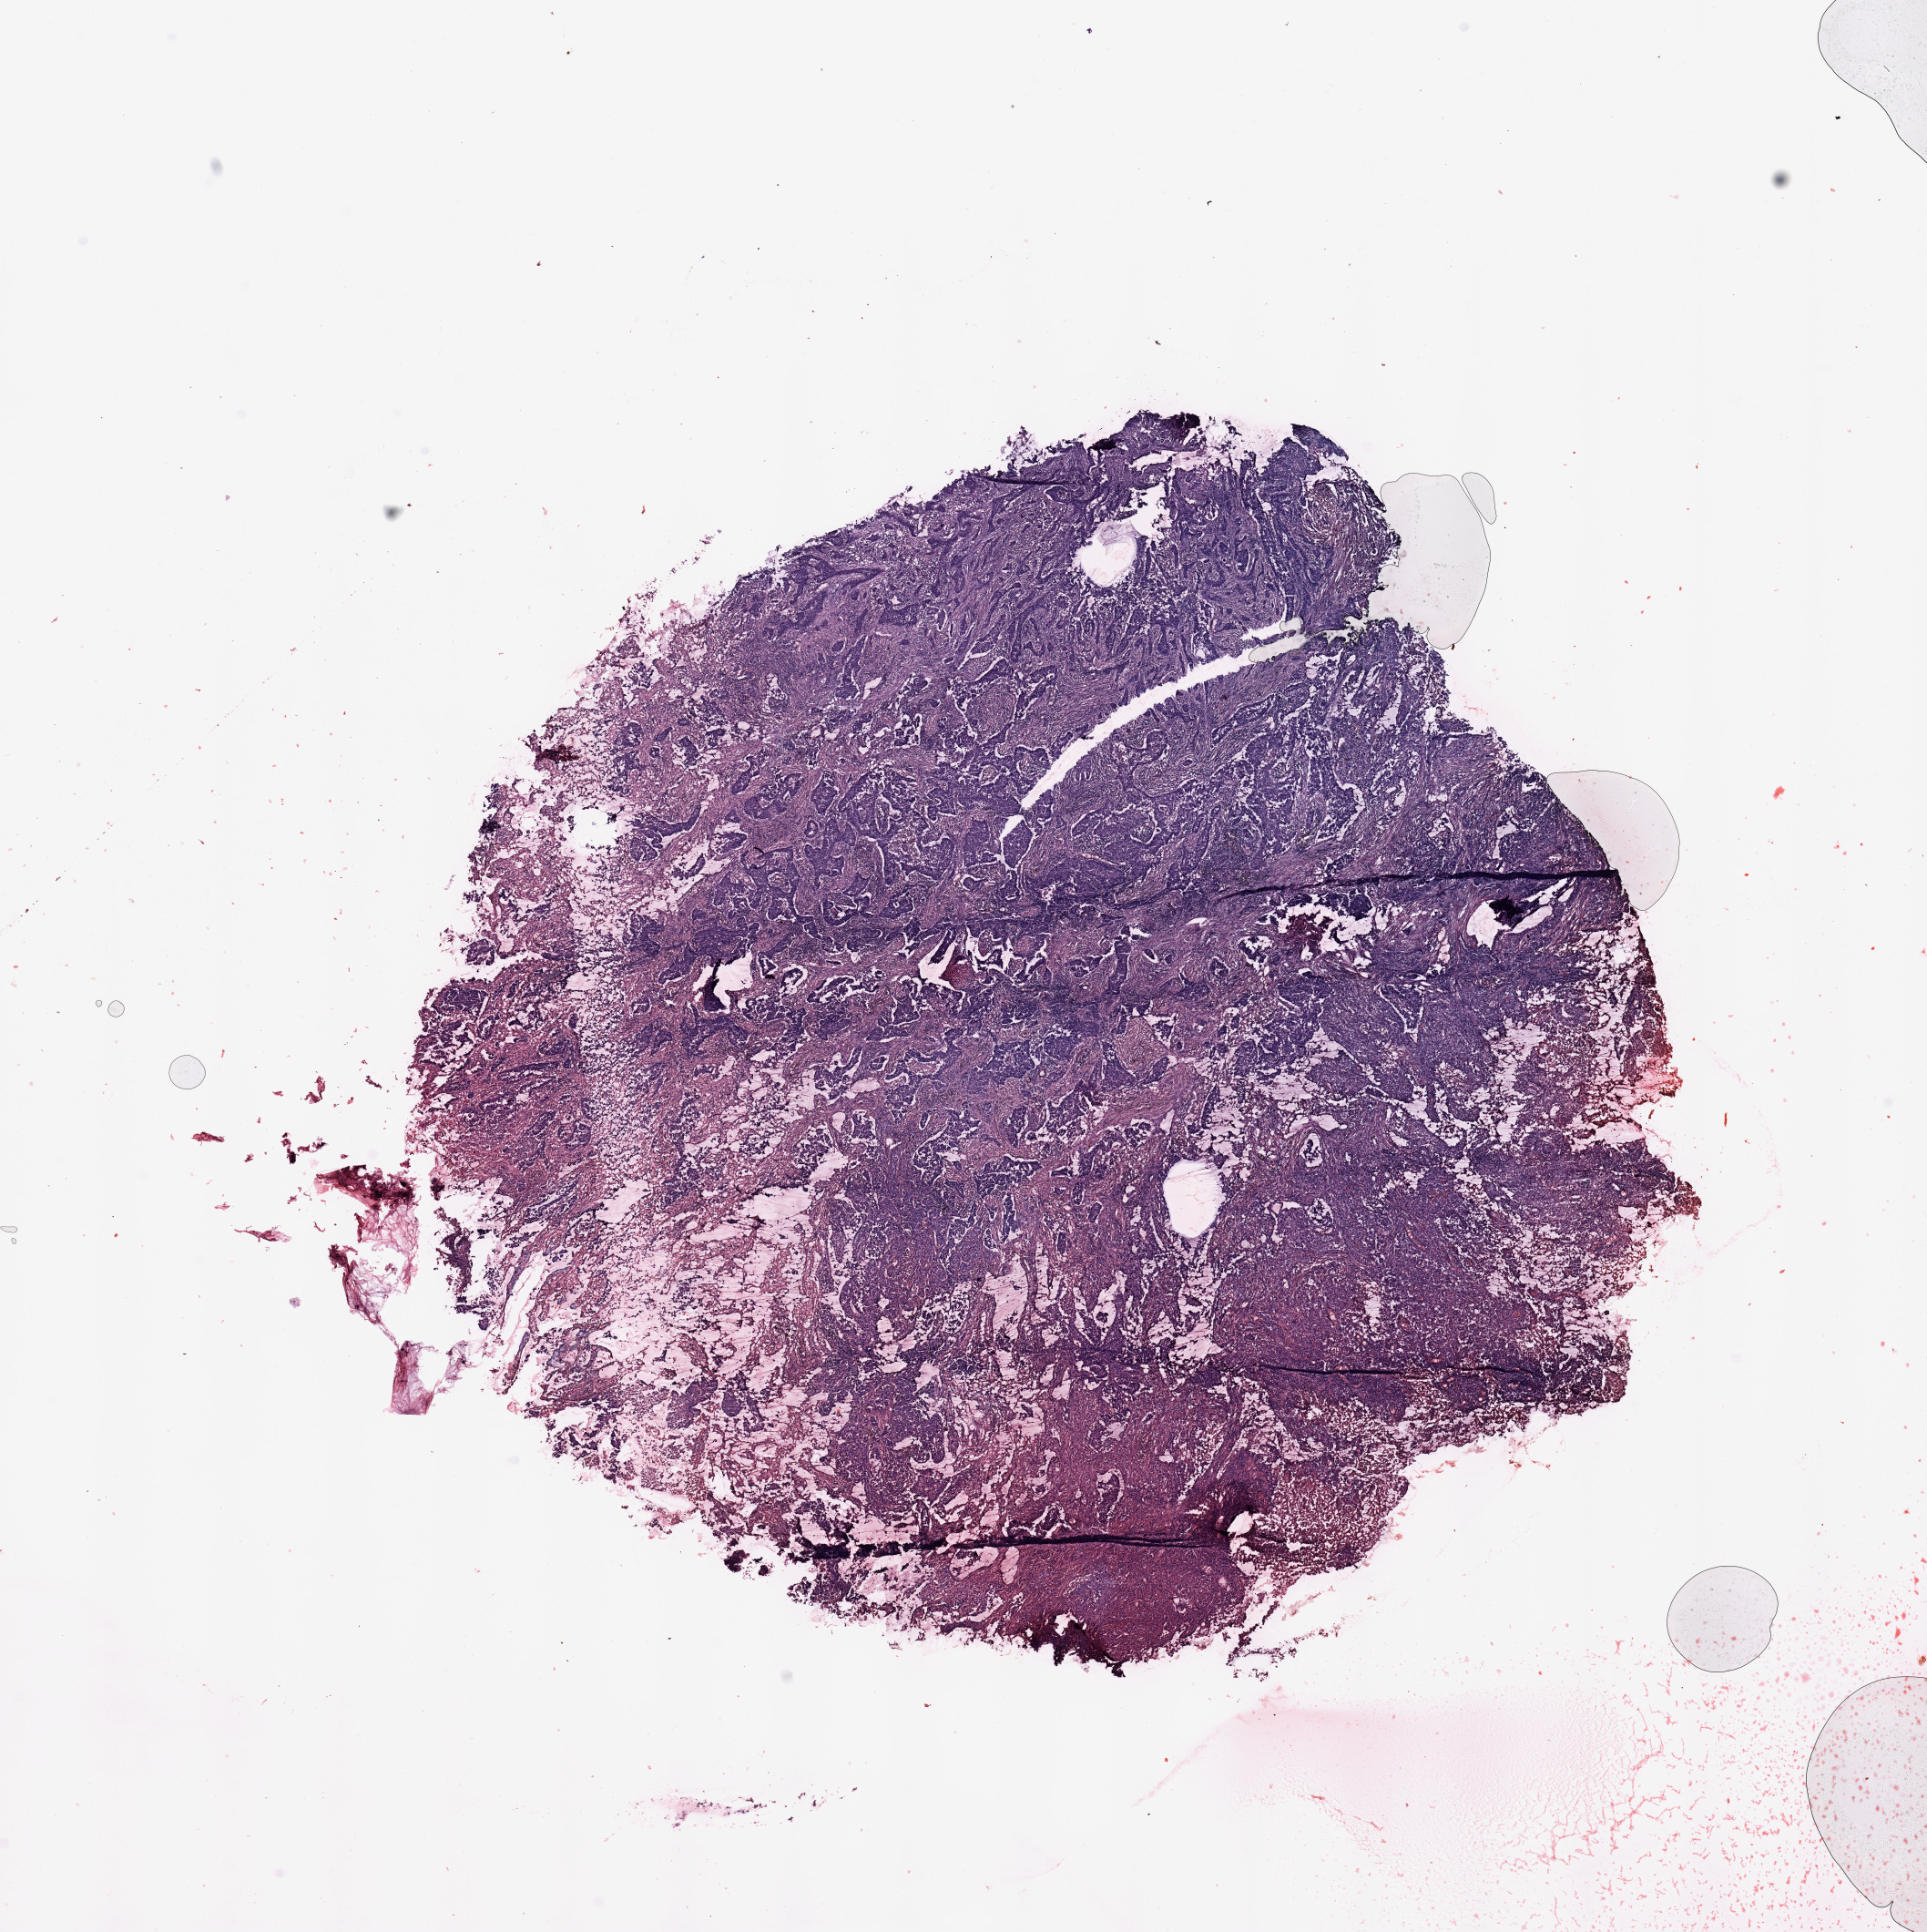
H&E whole-slide image, a low-resolution overview of the entire scanned area, about 16.7 x 16.8 mm (acquisition: 20x scan), tumour tissue sample, lung. Male, 67 y/o.
* primary tumour site (as recorded): left upper lobe
* patient diagnosis (cohort enrolment): squamous cell carcinoma (lung)